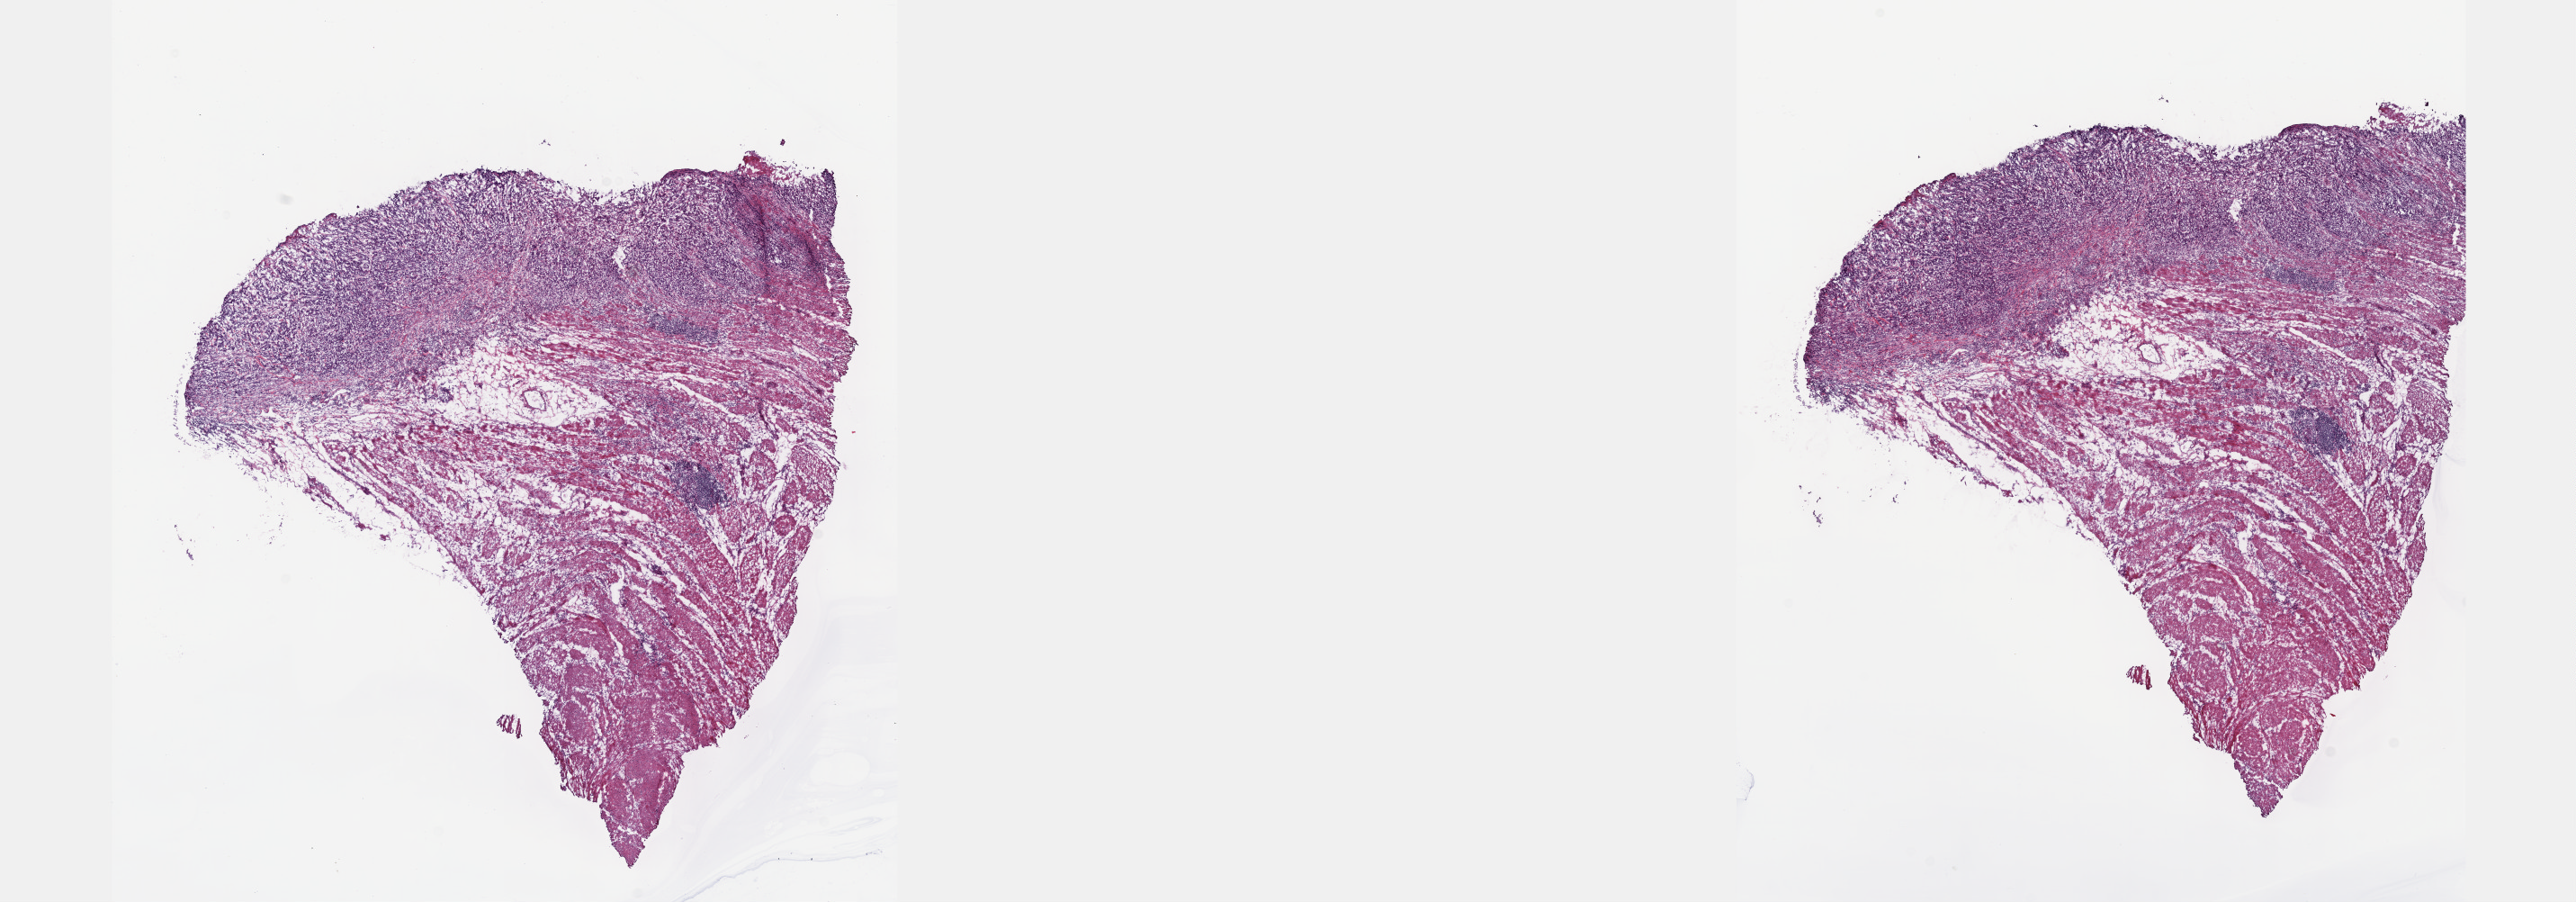
Whole-slide histology image, Hematoxylin and eosin (H&E) stained — low-resolution overview of the scanned area, about 23.1 x 8.1 mm (from a 40x scan), frozen section from the top of the tissue portion, stomach, primary tumour sample. Female patient; age at initial diagnosis 80 years. Histologic grade: G3 (poorly differentiated). Pathologist review of this section (percent, as recorded): tumour cells 50%, tumour nuclei 60%, normal cells 40%, stromal cells 10%, necrosis 0%. Inflammatory infiltration, as recorded: lymphocyte infiltration 0%, monocyte infiltration 0%, neutrophil infiltration 0%.
Lymph nodes positive (case pathology): 3 of 15 examined. Diagnosis: Carcinoma, diffuse type (cardia, NOS). AJCC pathologic stage: IIIA (6th edition). TNM: T3 N1 M0.